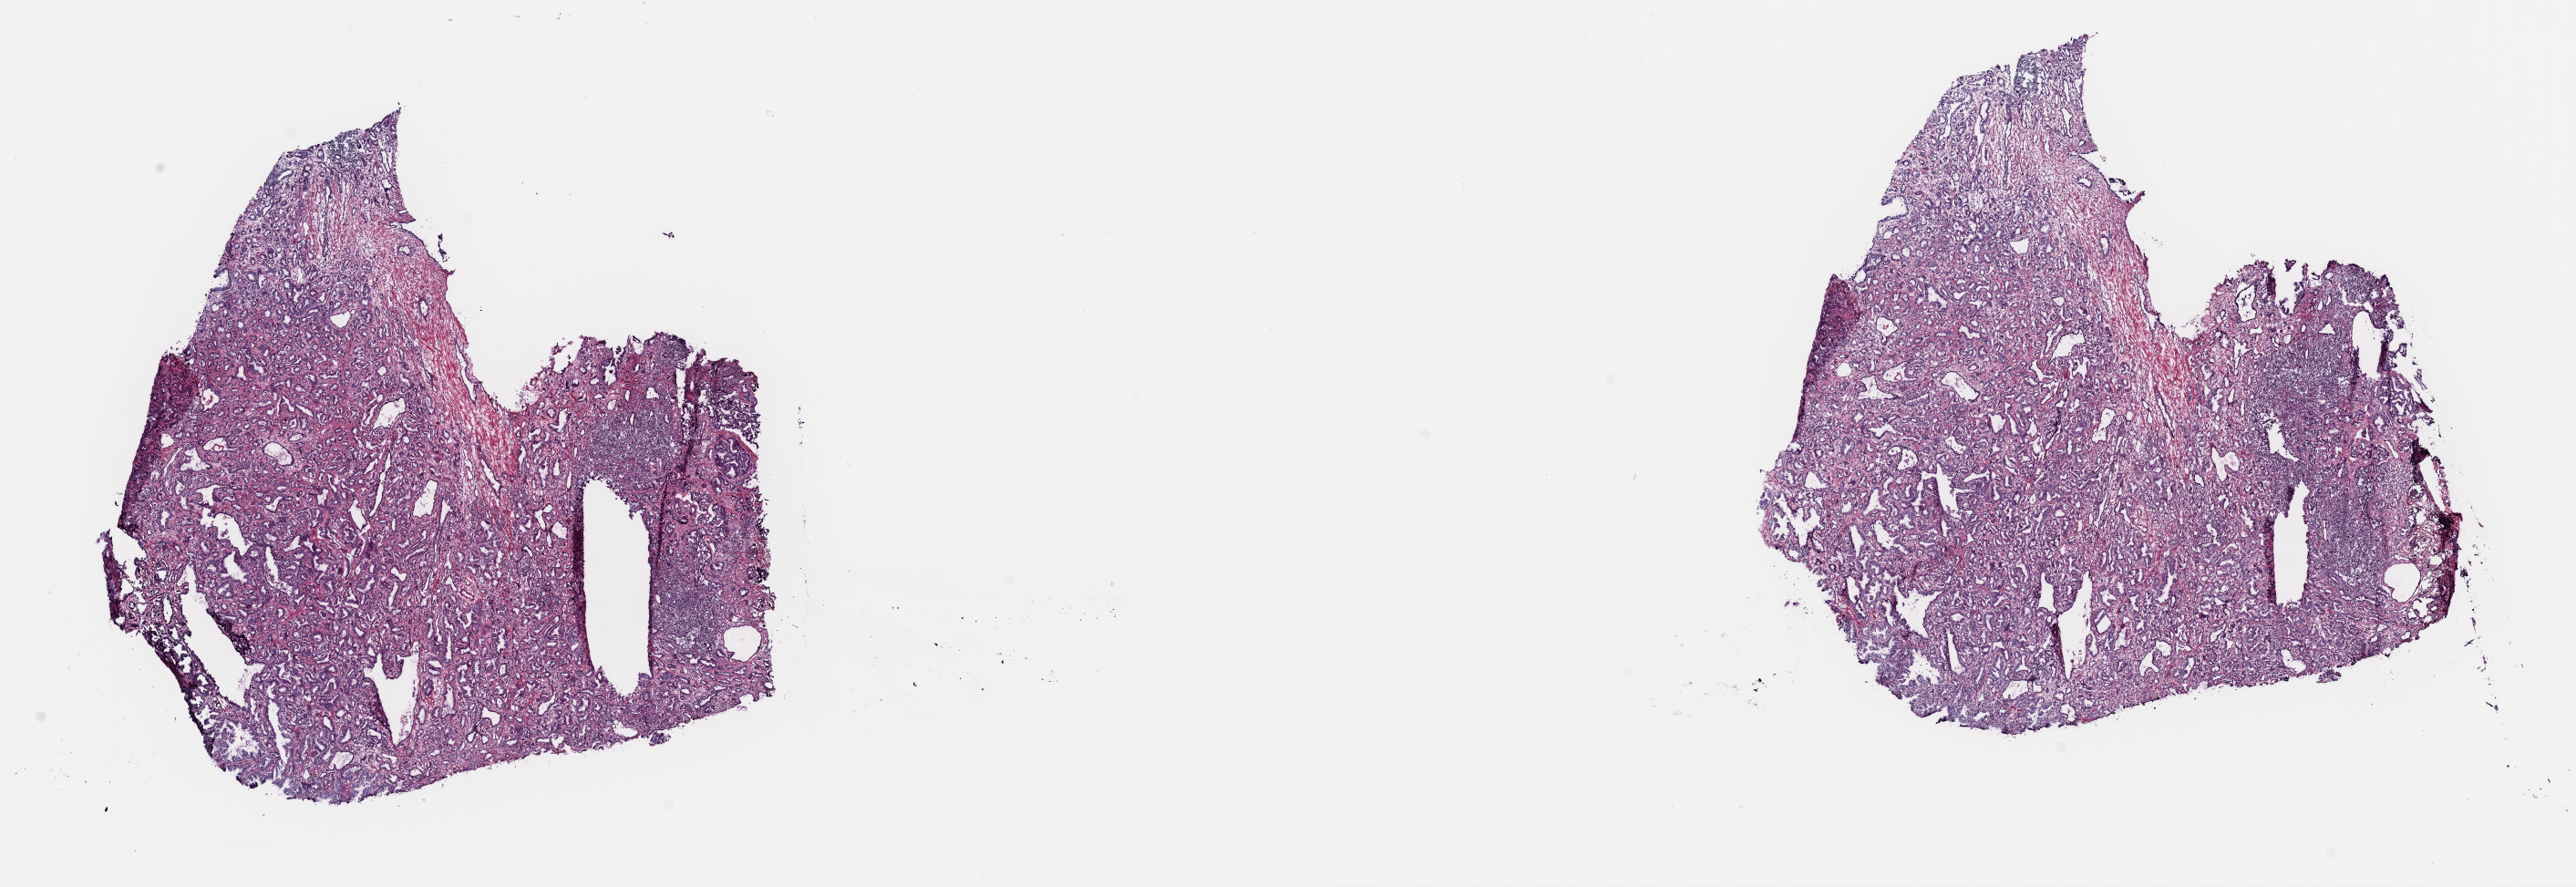
H&E-stained whole-slide image — shown as a low-resolution overview of the whole scanned area (about 22.3 x 7.7 mm), frozen section from the top of the tissue portion, prostate, primary tumour sample. Male, age 58 years at initial diagnosis. Gleason score: 7 (3+4). Pathologist review of this section (percent, as recorded): tumour cells 80%, tumour nuclei 90%, normal cells 0%, stromal cells 20%, necrosis 0%. Inflammatory infiltration, as recorded: lymphocyte infiltration 0%, monocyte infiltration 0%, neutrophil infiltration 0%.
Pathologic diagnosis: Adenocarcinoma, NOS (prostate gland).